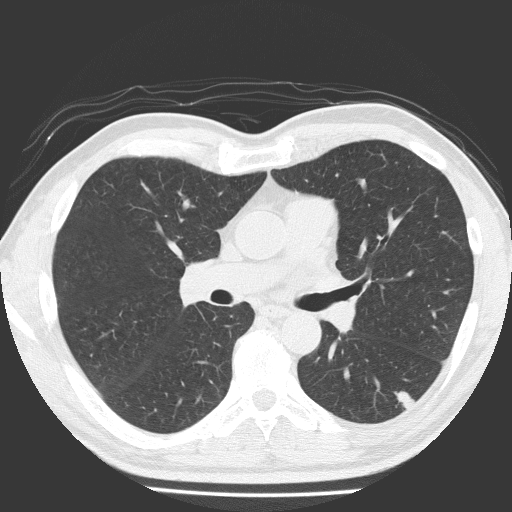
Axial slice from a low-dose chest CT screening exam. Baseline annual screen. Lung window (W 1500 / L -600 HU). Male, age 58 years at enrolment. Current smoker at enrolment.
Expert reader's lesion annotation, box from (x=364, y=373) to (x=427, y=422) px. The screening reader recorded 4 non-calcified nodules or masses ≥4 mm on this exam; which of them this box marks is not recorded. Official screen result: positive, change unspecified: nodule(s) >= 4 mm or enlarging nodule(s), mass(es), or other non-specific abnormalities suspicious for lung cancer. Later outcome: lung cancer diagnosed 99 days after this screen — adenosquamous carcinoma, left lower lobe, moderately differentiated (G2), stage IA (AJCC 6th edition), 28 mm at pathology.